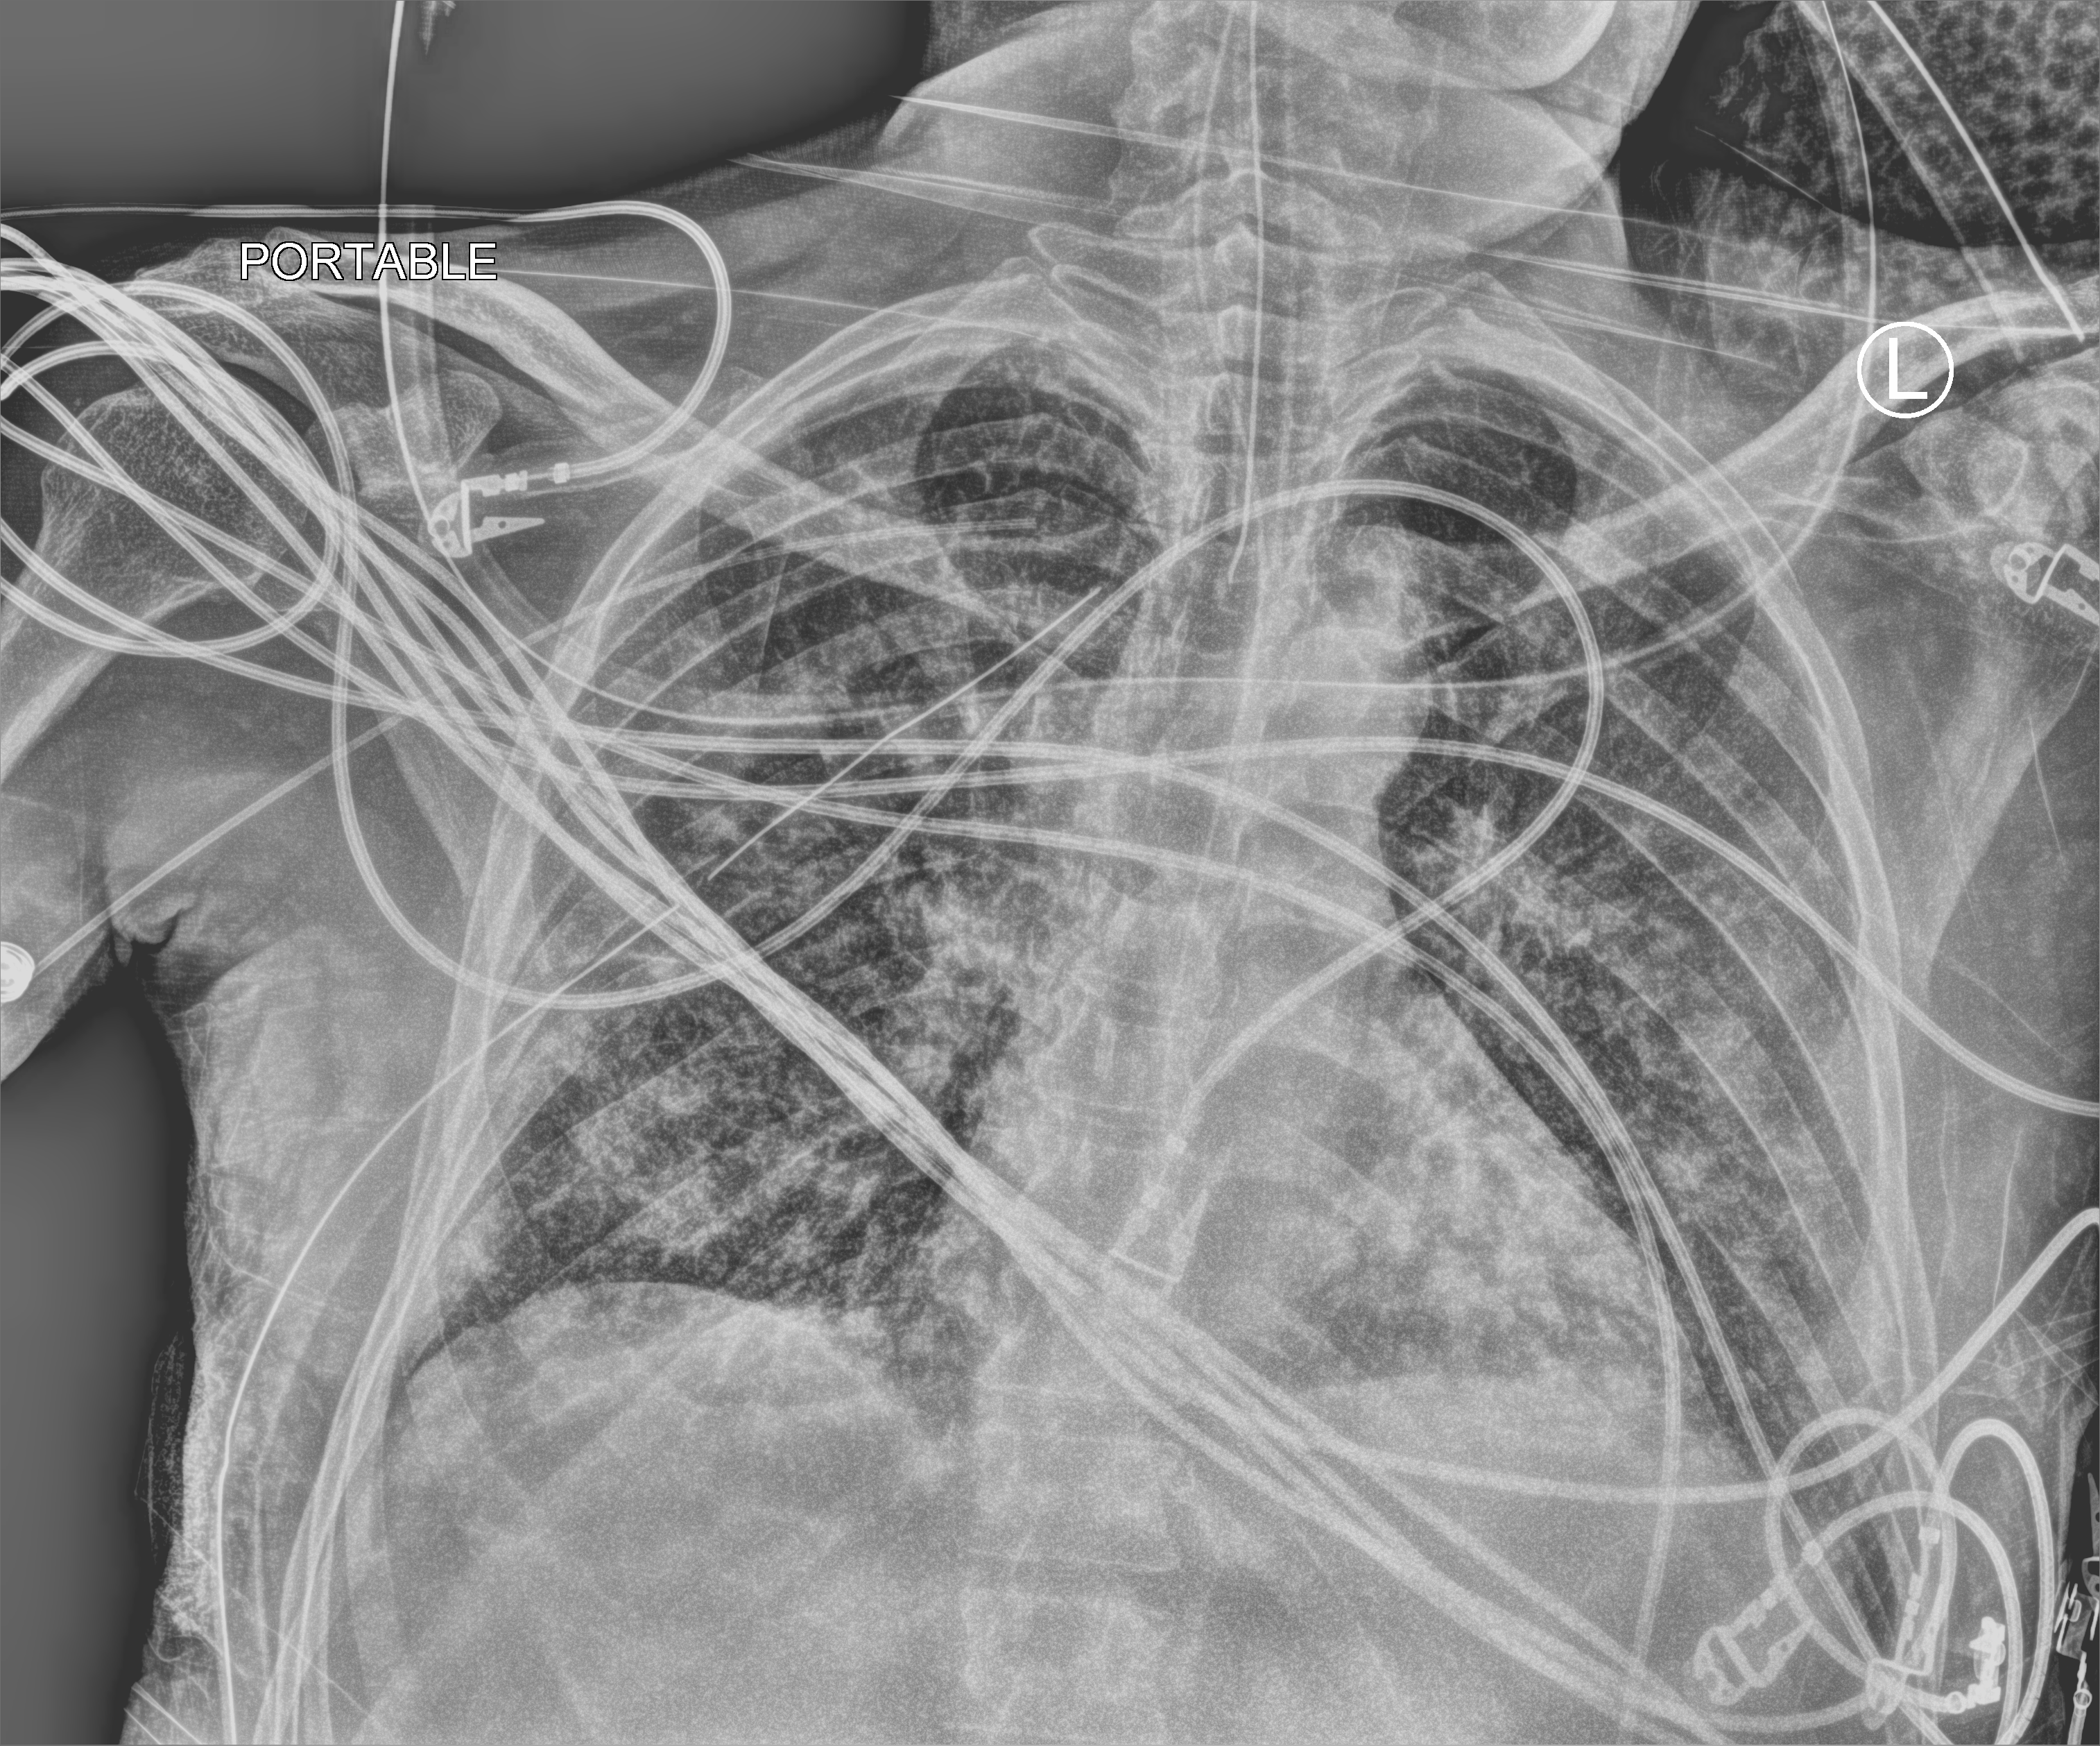
Bedside chest radiograph (computed radiography), anteroposterior (AP) projection. Male patient hospitalised with COVID-19, age 18–59 years.
Admission-level facts for this patient (not findings on this image; timing relative to this image not recorded): length of hospital stay: 41 days.